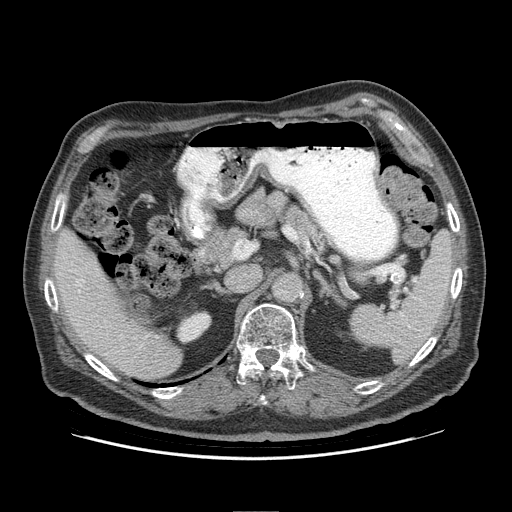
Contrast-enhanced abdominal CT (liver protocol), one axial slice. Position 53 of 95 along the scan axis. 140 kVp. Soft-tissue window (W 400 / L 40 HU). 2.5 mm slice thickness. 512 × 512 image matrix. Case-level facts recorded for this patient, not image findings: diagnosis: hepatocellular carcinoma (patient treated with transarterial chemoembolisation; whether this scan precedes or follows treatment is not stated here); TNM stage (as recorded): Stage-IVB; Child-Pugh class: A; tumour nodularity: uninodular.
Annotated regions visible in this slice (semi-automatic segmentation, software-assisted and operator-edited):
- liver parenchyma outside the tumour (the mass and vessels are separate outlines, so this box may not span the whole liver): bounding box [x1, y1, x2, y2] px = [54, 228, 182, 378]